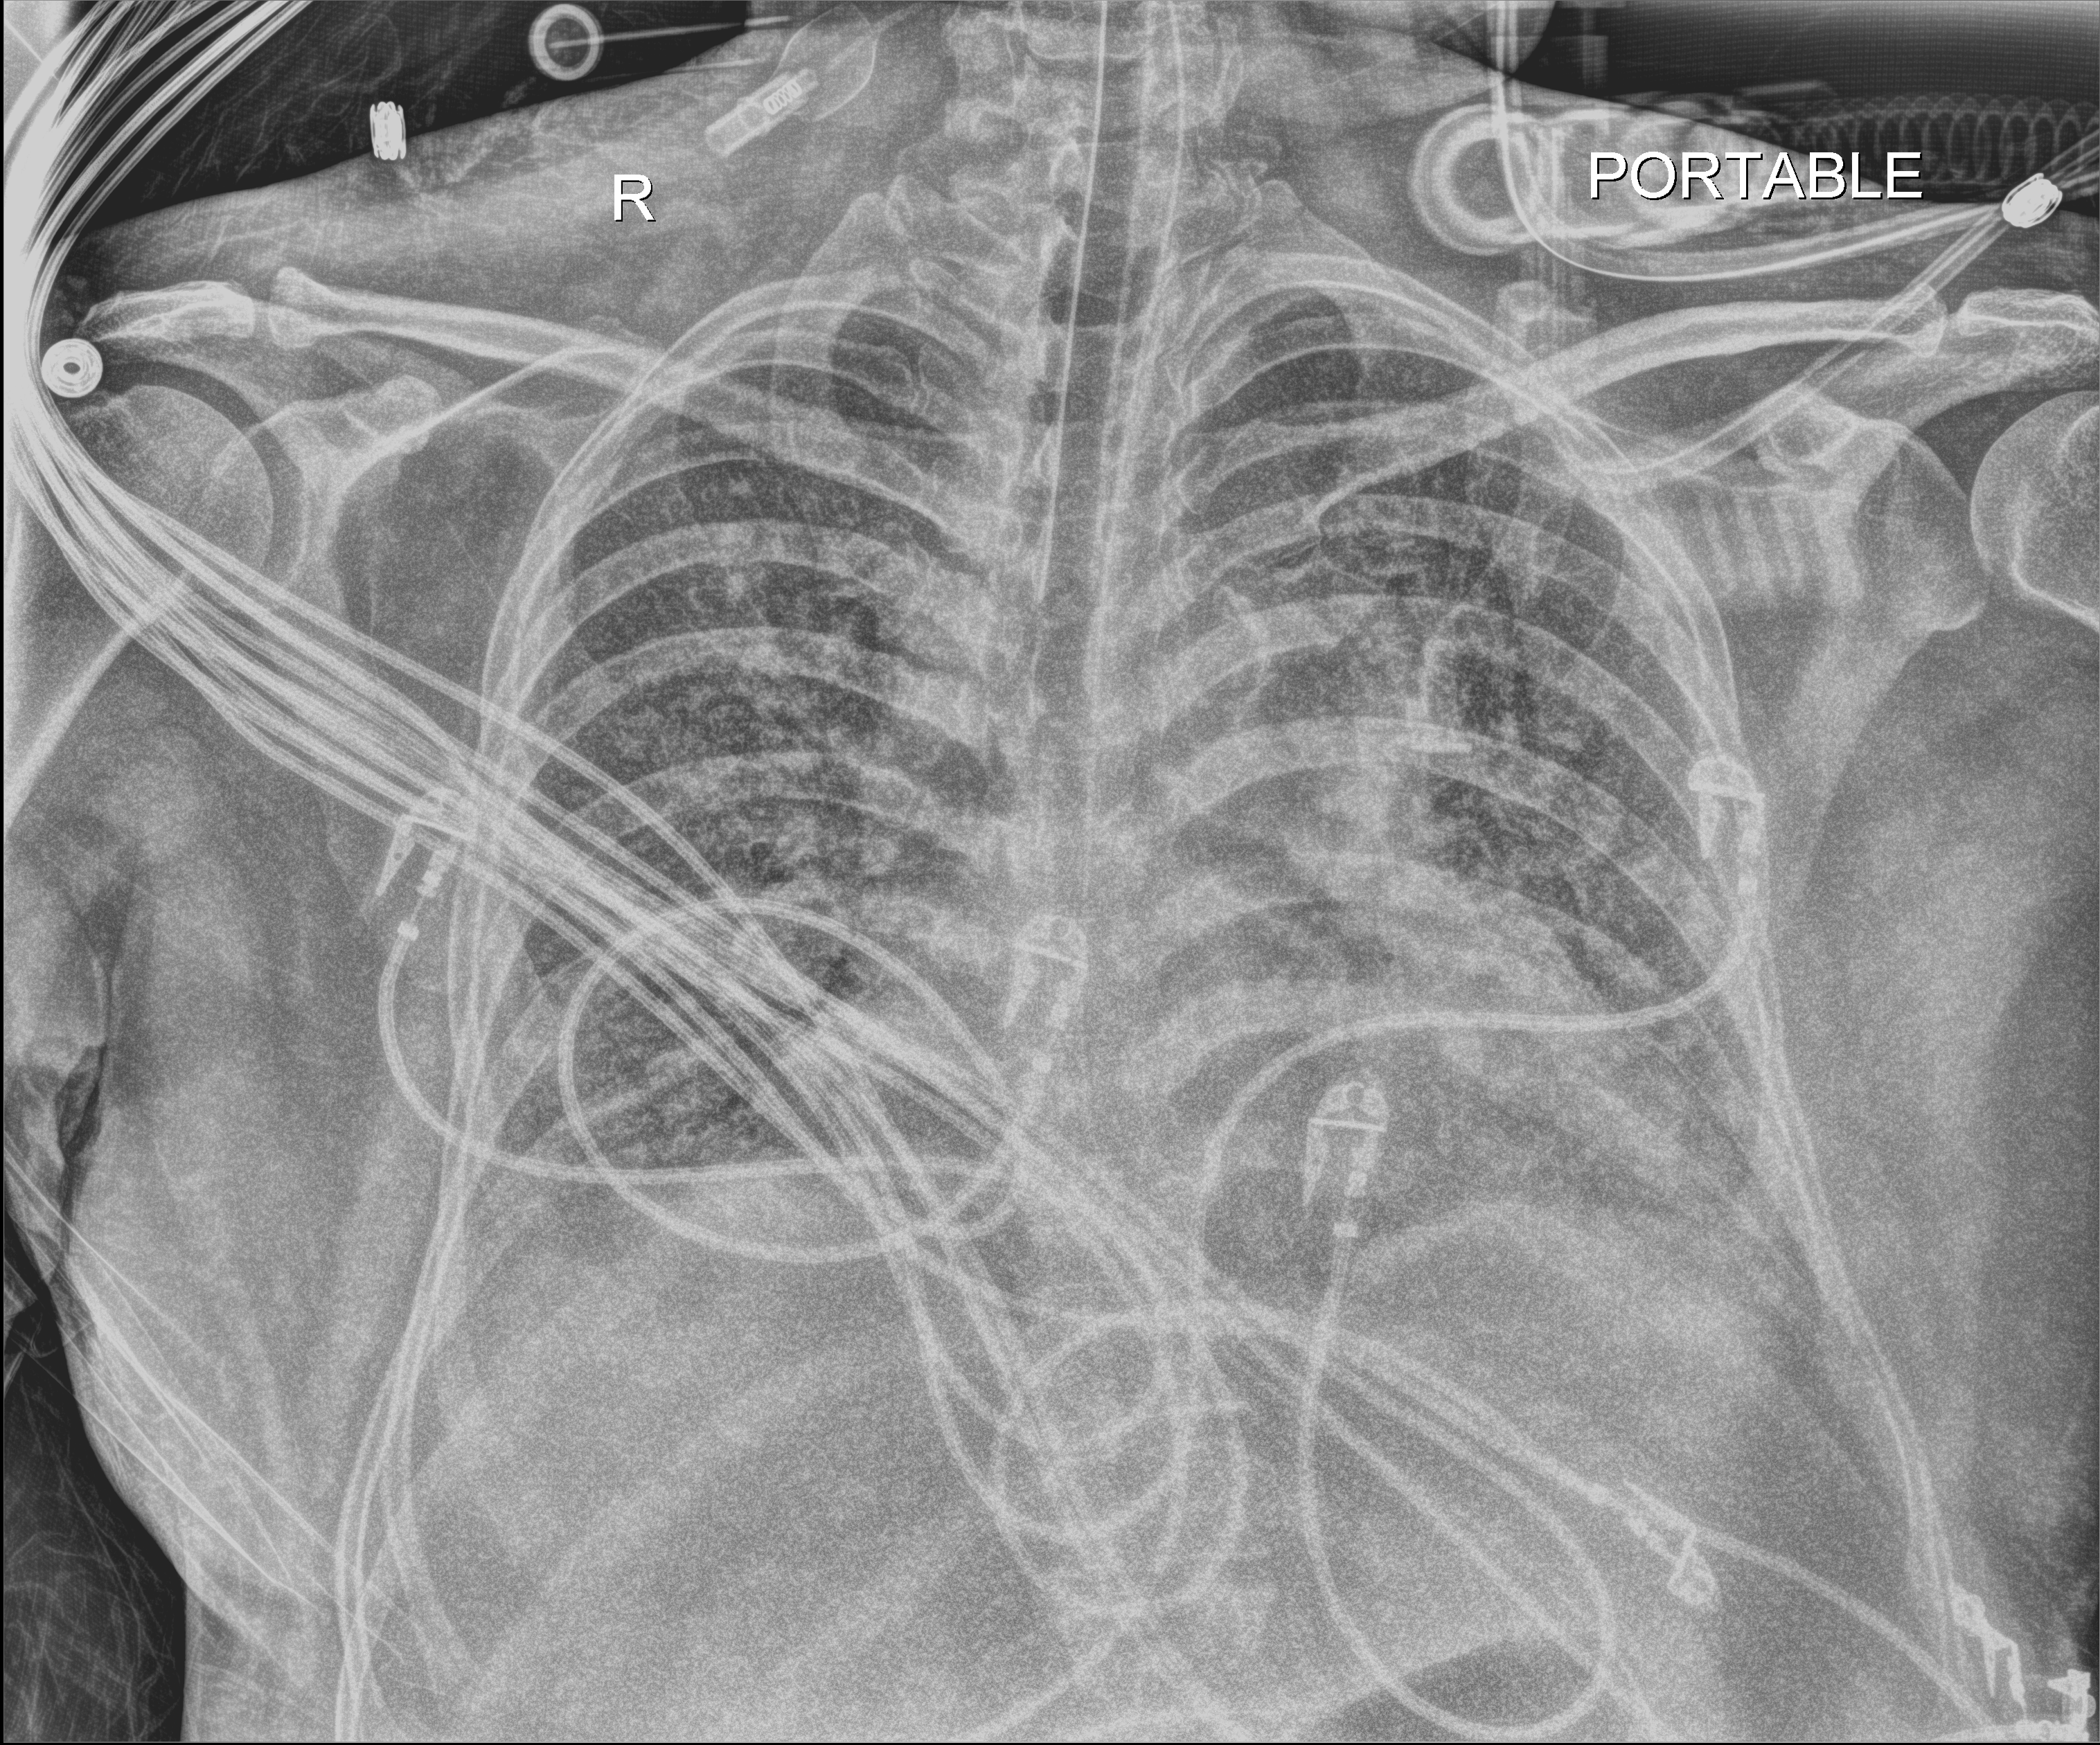
Chest X-ray (portable); anteroposterior (AP) projection. Adult patient hospitalised with COVID-19, age 18–59 years.
Hospital-stay facts (about this admission, not read from this image; timing relative to this image not recorded):
- COPD (admission record): no
- mechanically ventilated during this hospital stay: yes
- hypertension (admission record): no